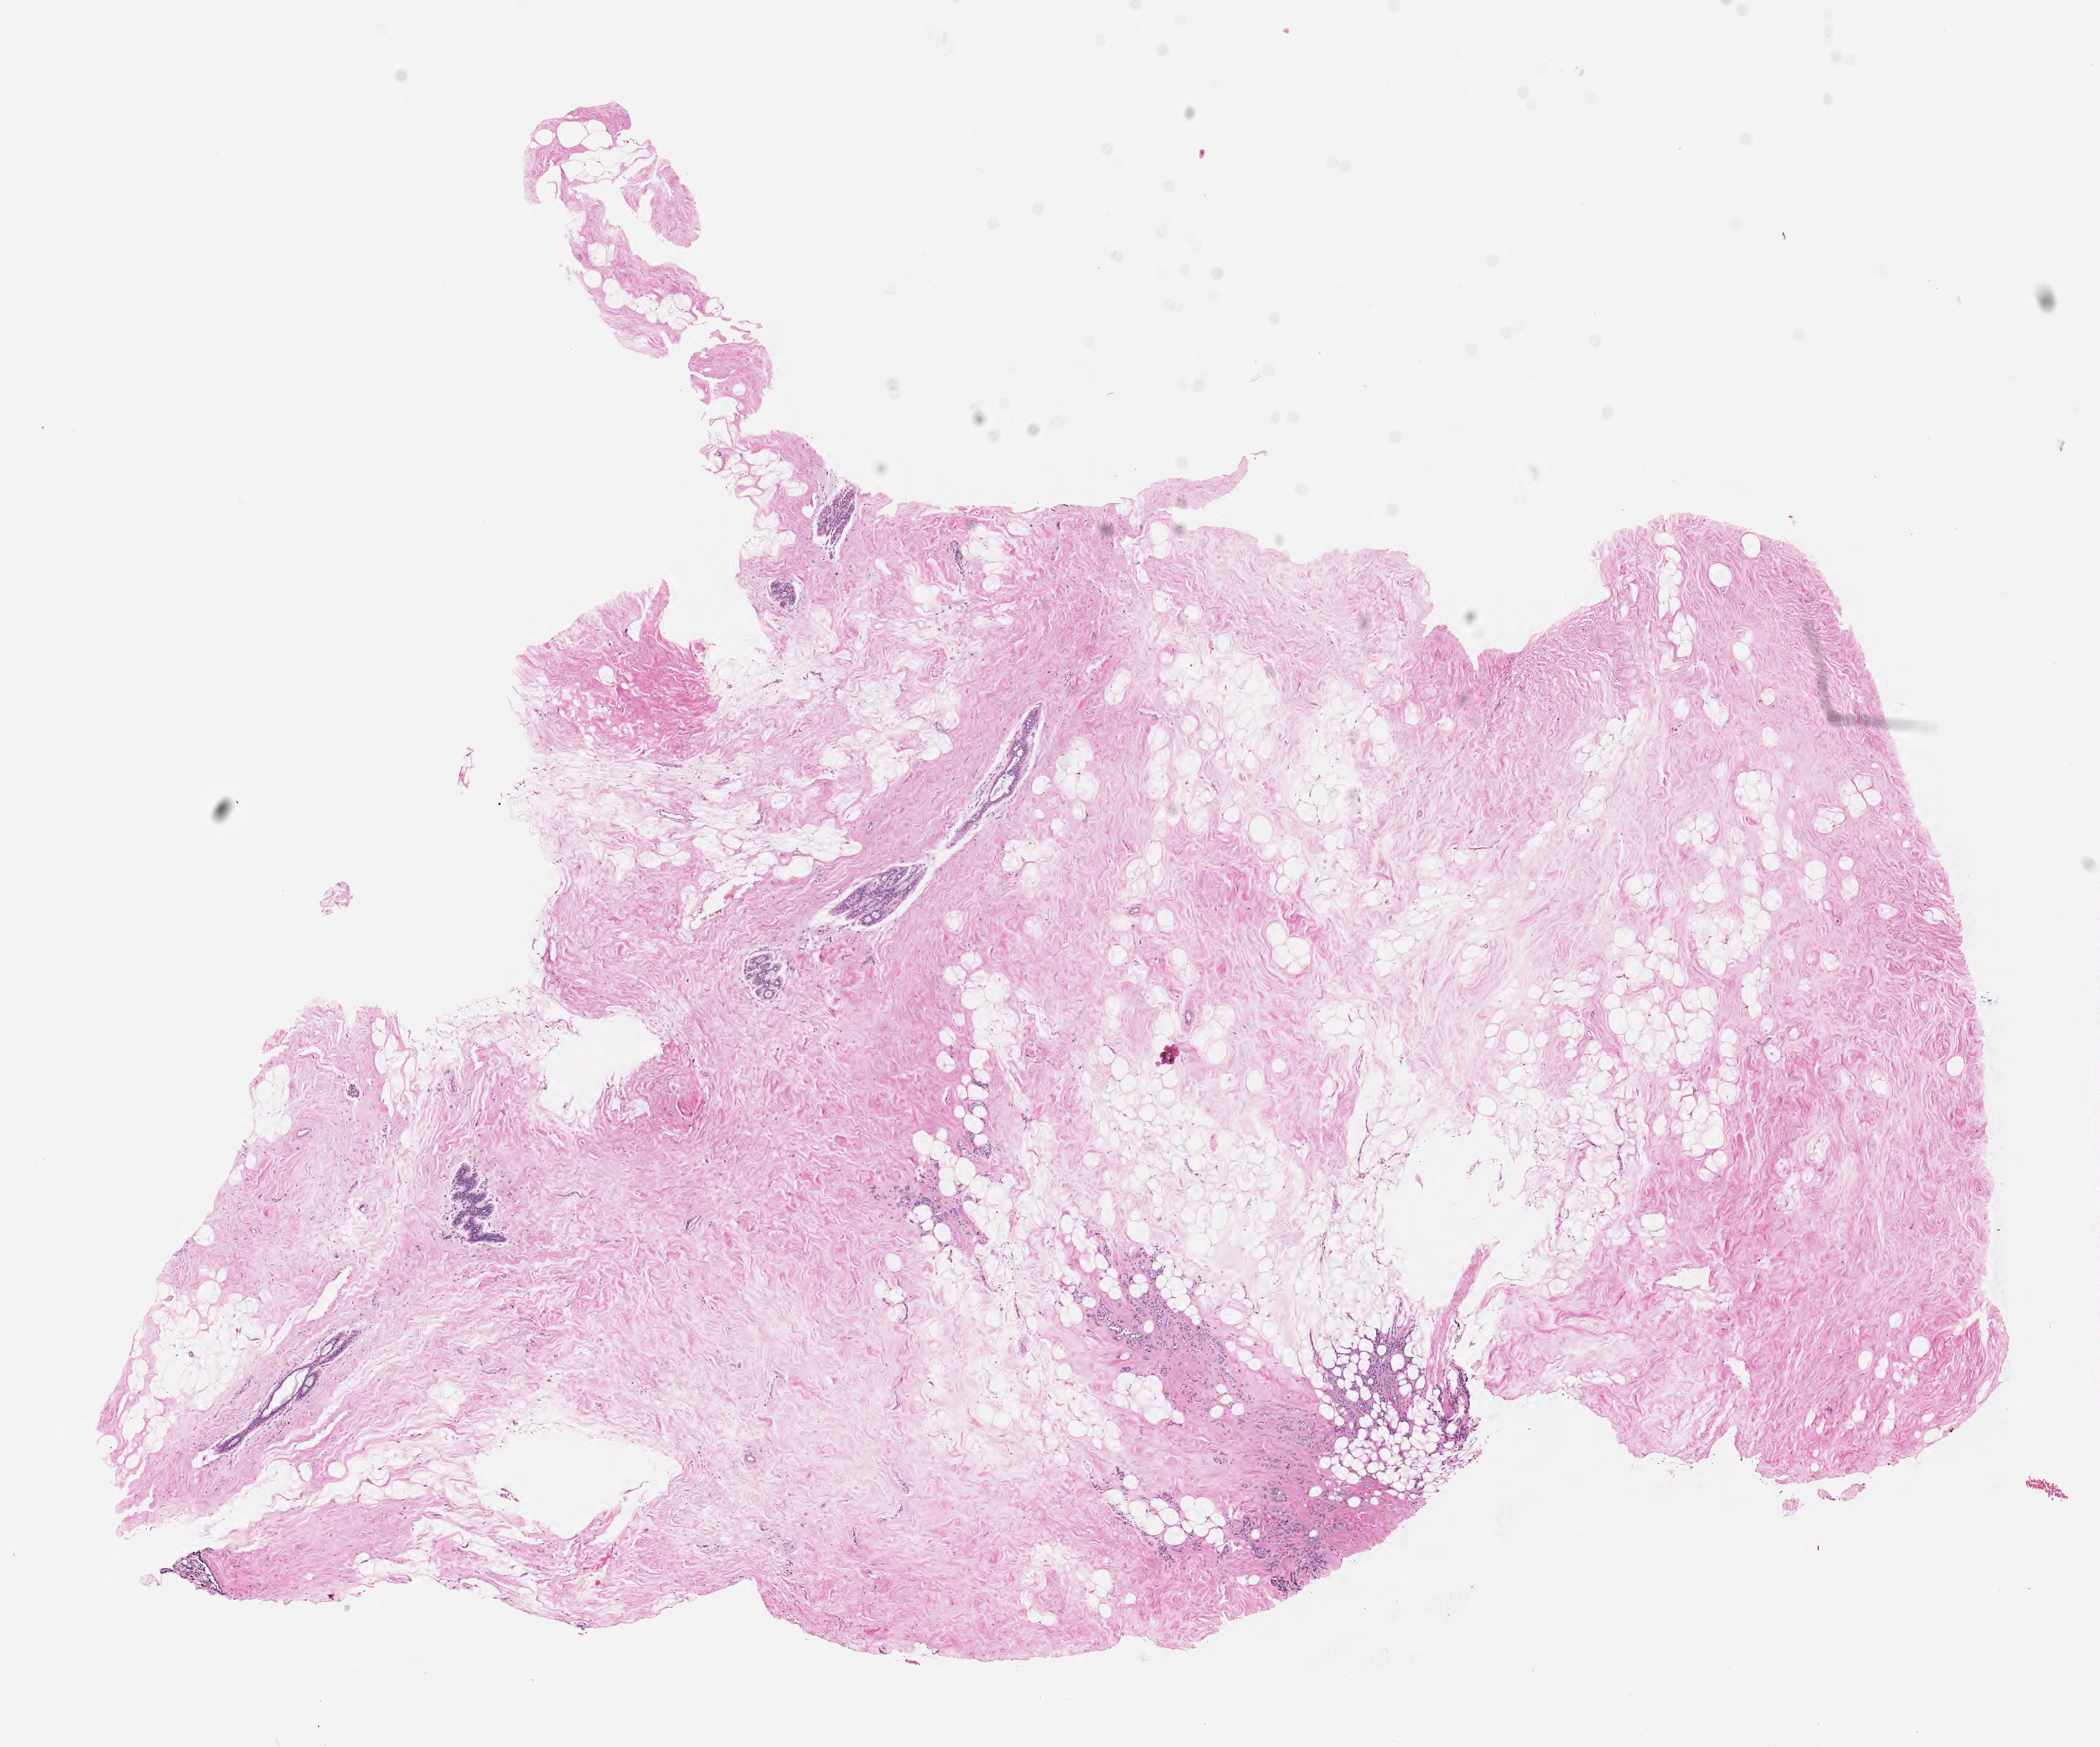
Digitized H&E-stained section, shown as a low-resolution overview of the whole scanned area (about 11.6 x 9.6 mm); formalin-fixed paraffin-embedded section; primary tumor; site: breast. Patient: female, age at initial diagnosis 57 years. Tumor grade: G2 (moderately differentiated). Slide review estimates, as recorded: tumor cells 3%, tumor nuclei 60%, stromal cells 95%, necrosis 0%, normal cells 2%. Infiltration values recorded for this section: lymphocyte infiltration 6%, monocyte infiltration 0%, neutrophil infiltration 0%.
AJCC pathologic stage: Stage IIA. Histologic diagnosis: Lobular carcinoma, NOS. Section: bottom of the tissue portion.